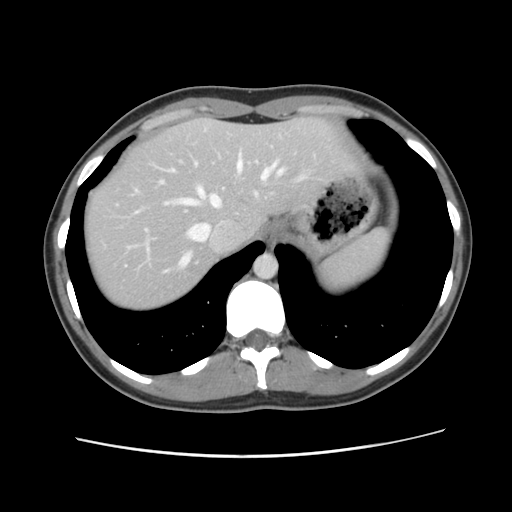
Contrast-enhanced abdominal CT, one axial slice; position 98 of 134 along the scan axis; 120 kVp; intravenous contrast given; soft-tissue window (W 400 / L 40 HU); 2.5 mm slice thickness; 512 × 512 image matrix, field of view 339 × 339 mm. Female patient, age 33 years. Case-level facts recorded for this patient, not image findings: diagnosis: colorectal cancer liver metastases, imaged before liver resection; multiple liver metastases: yes; largest metastasis: 4.5 cm; chemotherapy before resection: no.
Outlined on this slice (outlined manually by an expert reader):
- hepatic veins: box from (x=135, y=157) to (x=305, y=267) px
- liver: (x=83, y=117)–(x=353, y=312)
- planned liver remnant (the part of the liver to remain after resection): (x=84, y=117)–(x=355, y=312)
- portal vein (with intrahepatic branches): (x=115, y=203)–(x=153, y=251)